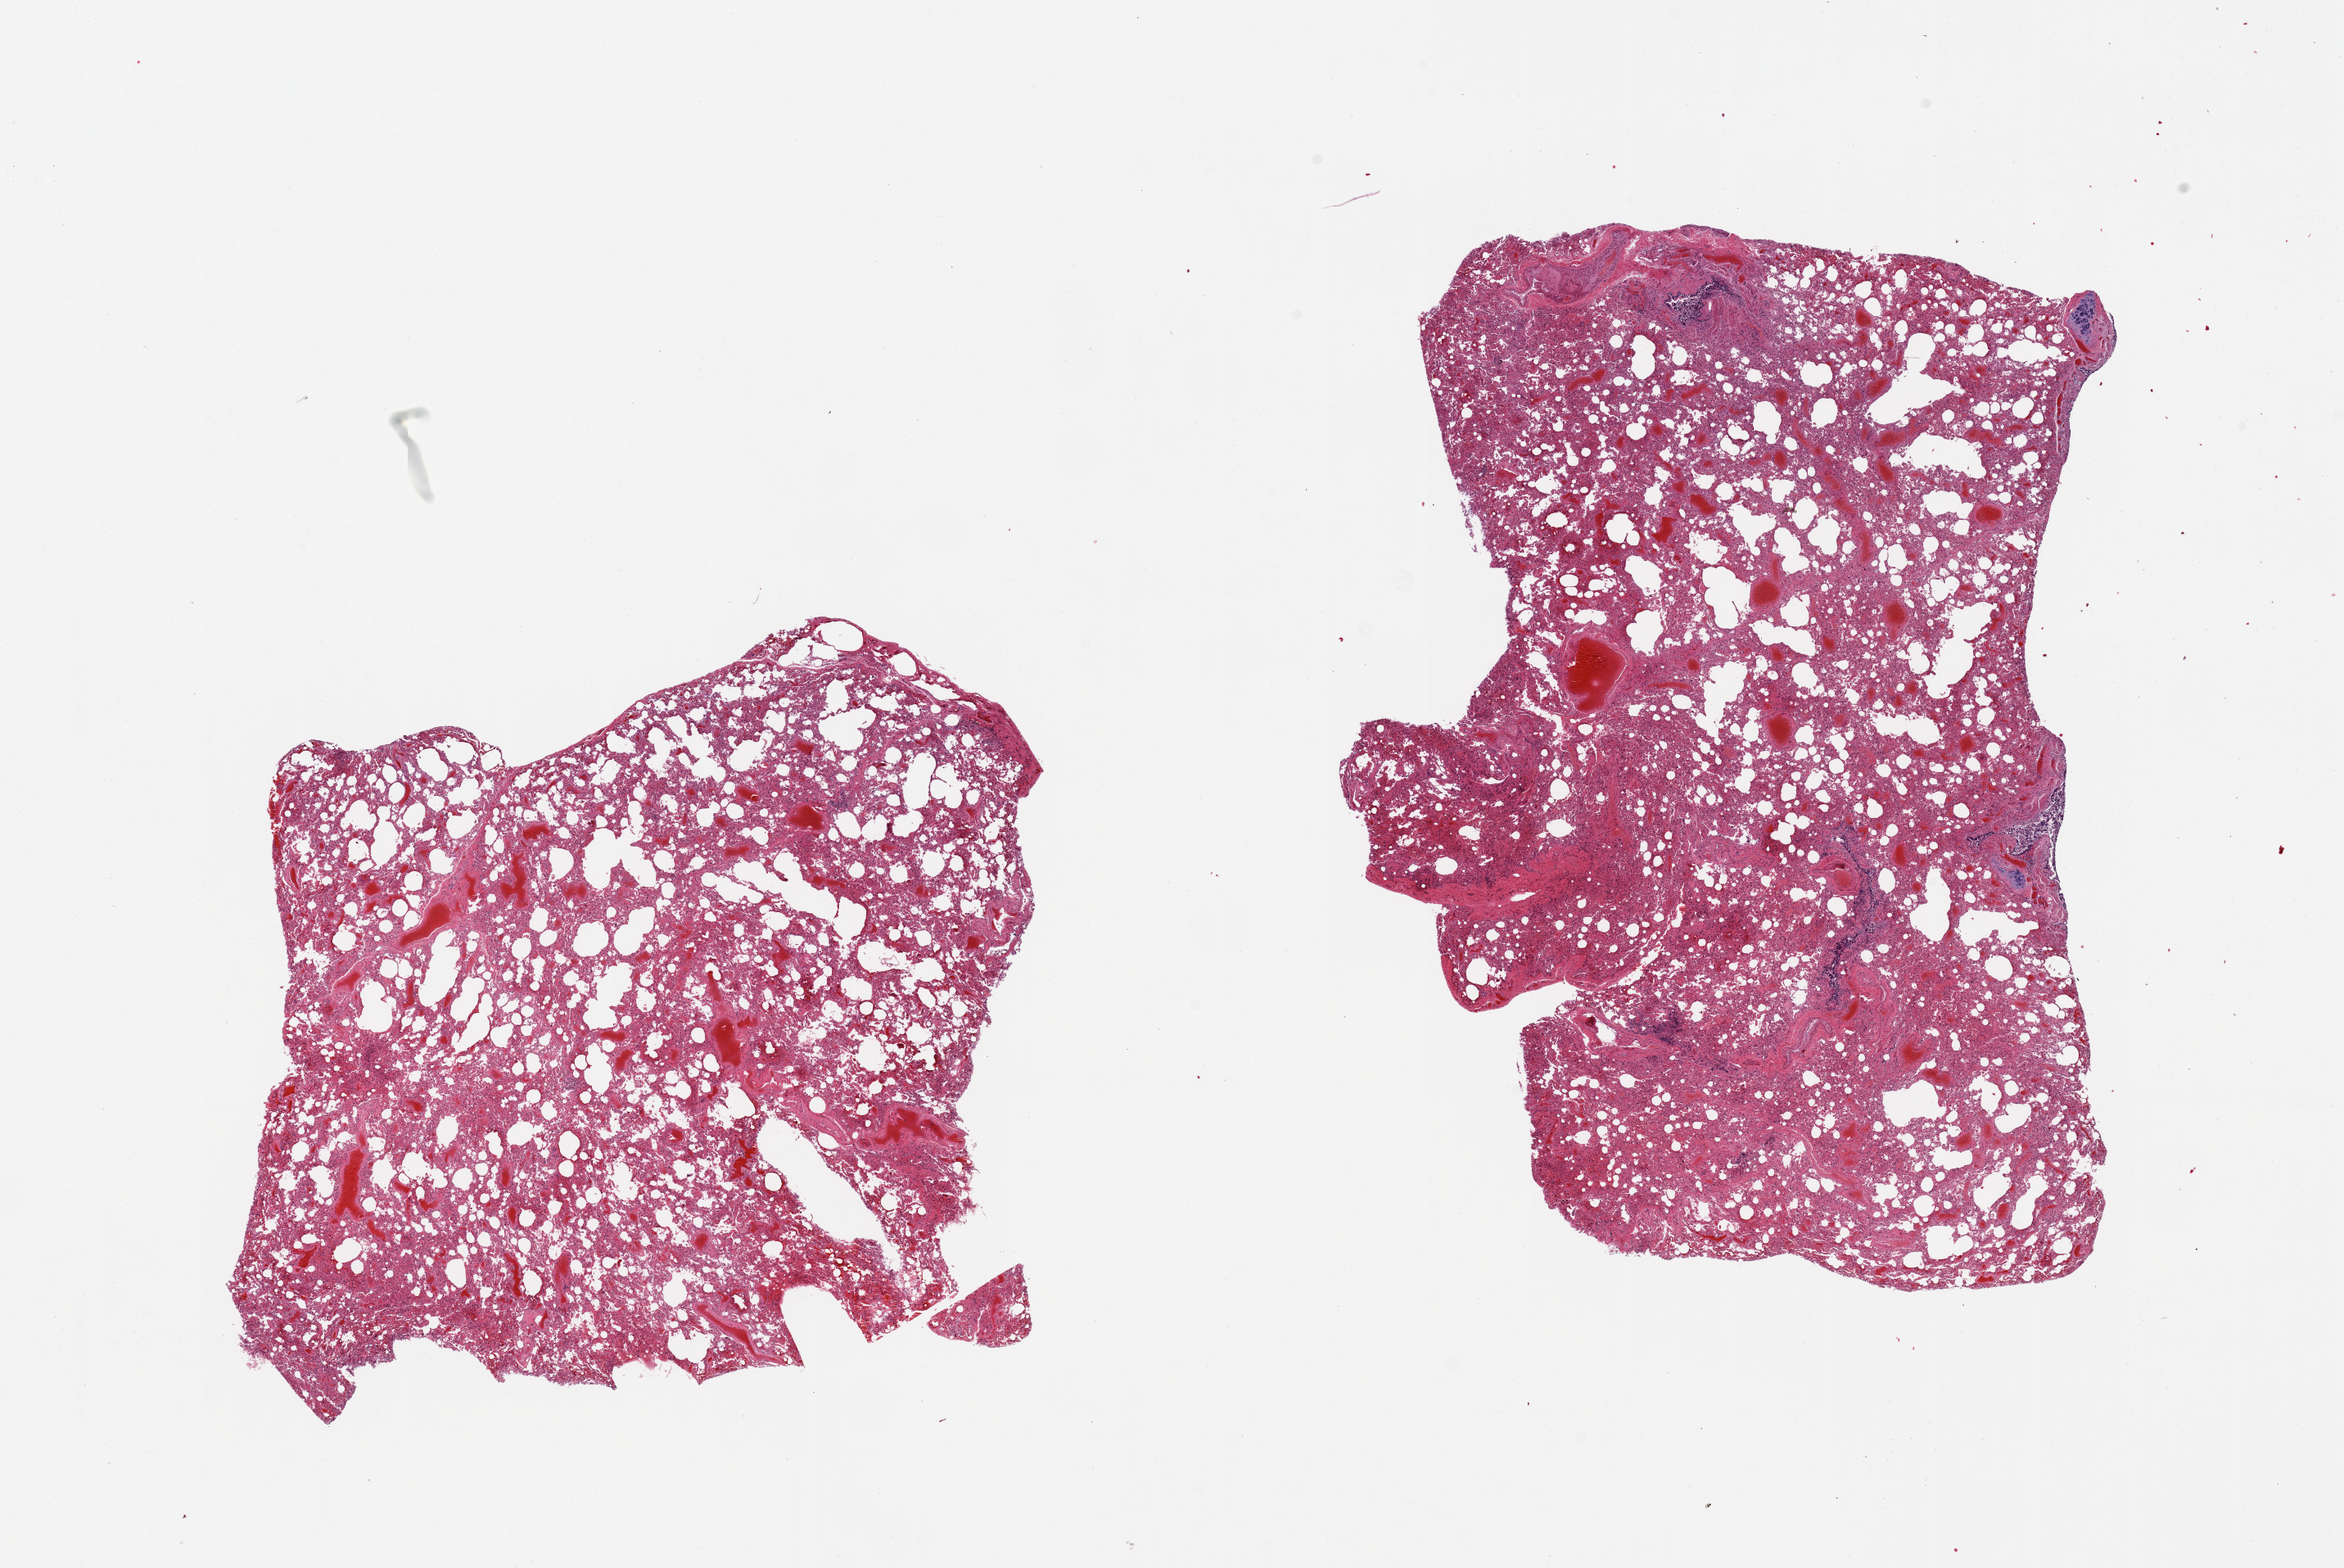
Whole-slide image, H&E stain — shown as a low-resolution overview of the whole scanned area (about 22.6 x 15.1 mm, from a 20x scan), PAXgene-fixed, paraffin-embedded tissue, sampled site (target tissue): lung, donor tissue sample. Female donor.
* pathologist's review note for this sample: 2 pieces moderate/marked congestion/edema; foci of pneumonia and probably fibrosis